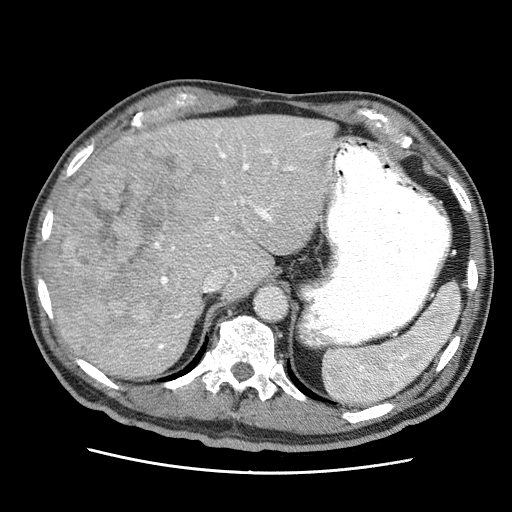
Contrast-enhanced abdominal CT (liver protocol), one axial slice. Position 41 of 75 along the scan axis. Reconstruction kernel STANDARD. Soft-tissue window (W 400 / L 40 HU). 2.5 mm slice thickness. 512 × 512 image matrix. From the clinical record (not read from this slice): diagnosis: hepatocellular carcinoma (patient treated with transarterial chemoembolisation; whether this scan precedes or follows treatment is not stated here); TNM stage (as recorded): Stage-IIIA; Child-Pugh class: A; tumour size: 13.9 cm.
Structures marked on this image (semi-automatically segmented with operator editing):
- liver parenchyma outside the tumour (the mass and vessels are separate outlines, so this box may not span the whole liver): box from (x=47, y=114) to (x=334, y=376) px
- mass: (x=49, y=142)–(x=224, y=348)
- liver vessels: (x=120, y=129)–(x=332, y=357)